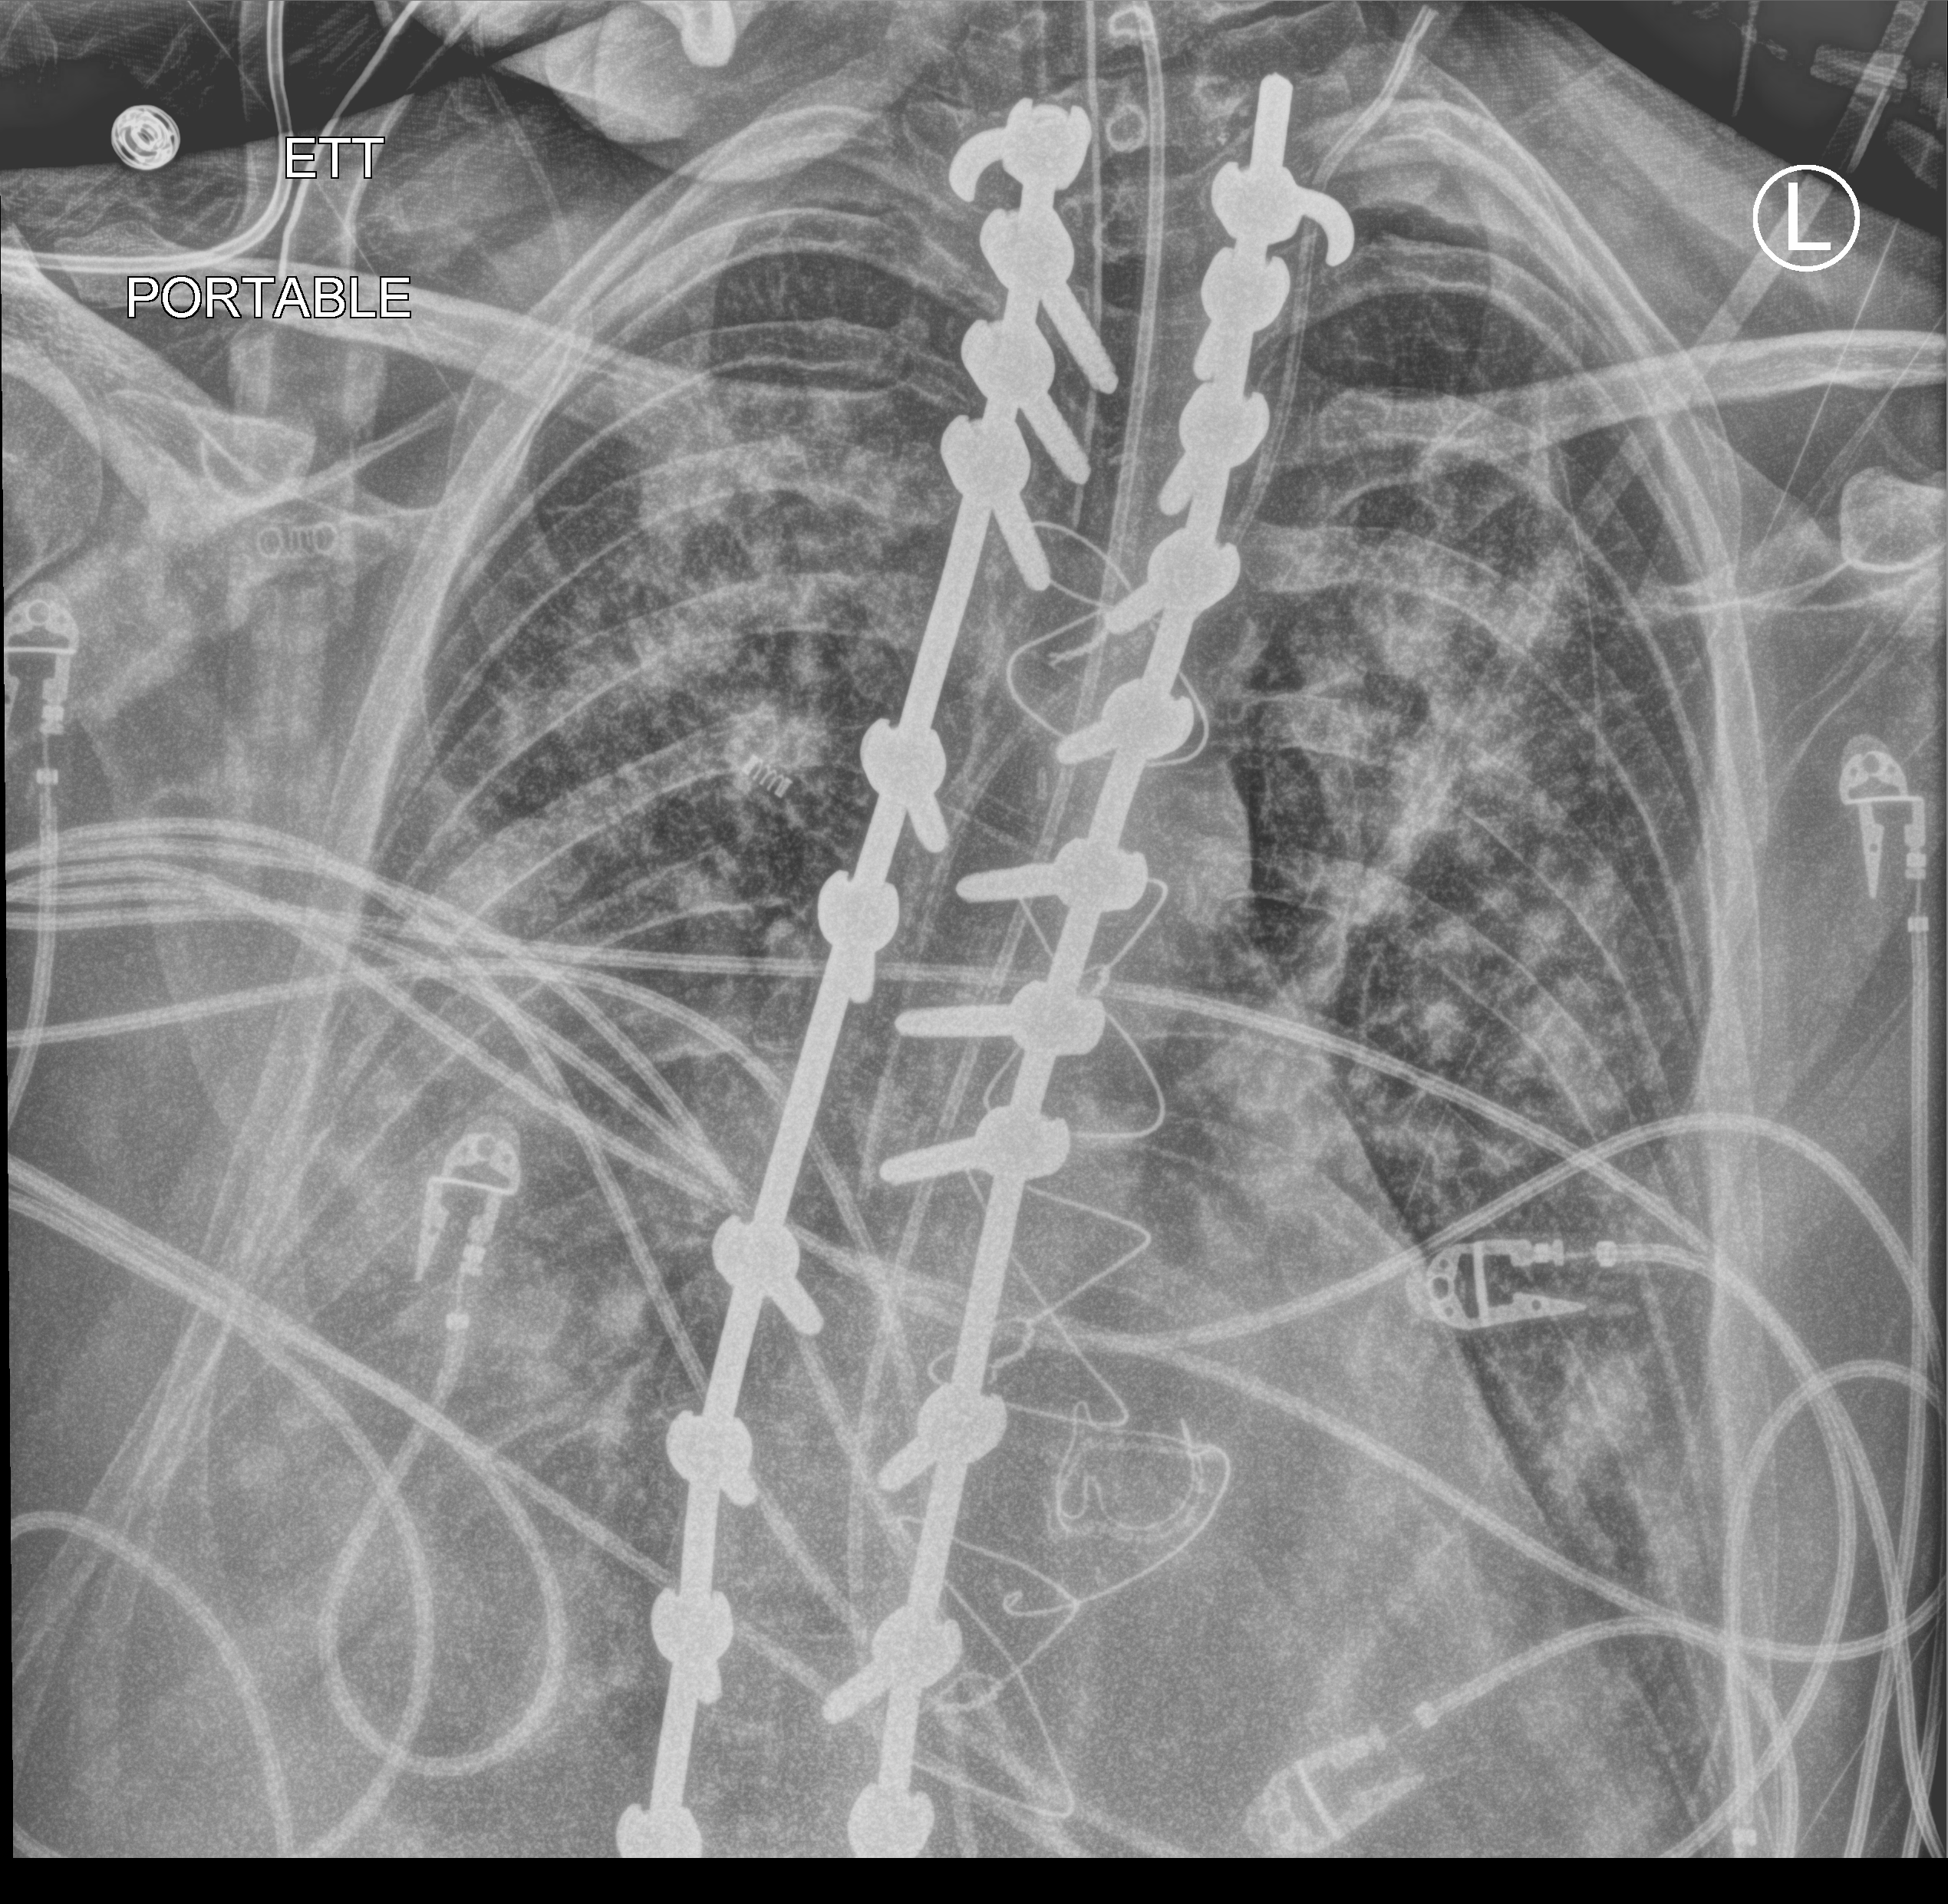
Portable chest radiograph. Patient hospitalised with COVID-19, aged 18–59 years.
From the hospital-stay record, not from the radiograph (when in the stay this image was taken is not recorded): COPD (admission record): no; mechanically ventilated during this hospital stay: yes.